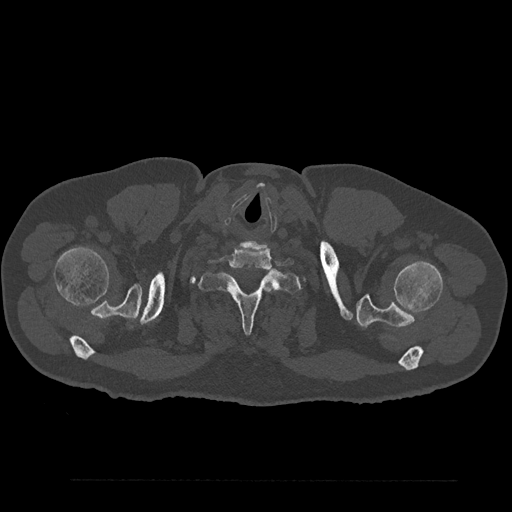
CT including the spine, one axial slice; position 762 of 797 along the scan axis; reconstruction kernel Br40s/3; bone window (W 1800 / L 400 HU); 0.5 mm slice thickness; 512 × 512 image matrix. Patient: male, 61 years. Case-level facts recorded for this patient, not image findings: primary cancer: prostate.
Annotated regions visible in this slice (semi-automatically segmented with operator editing):
- T1 vertebra: bounding box <198,261,301,334> (left, top, right, bottom; pixels)